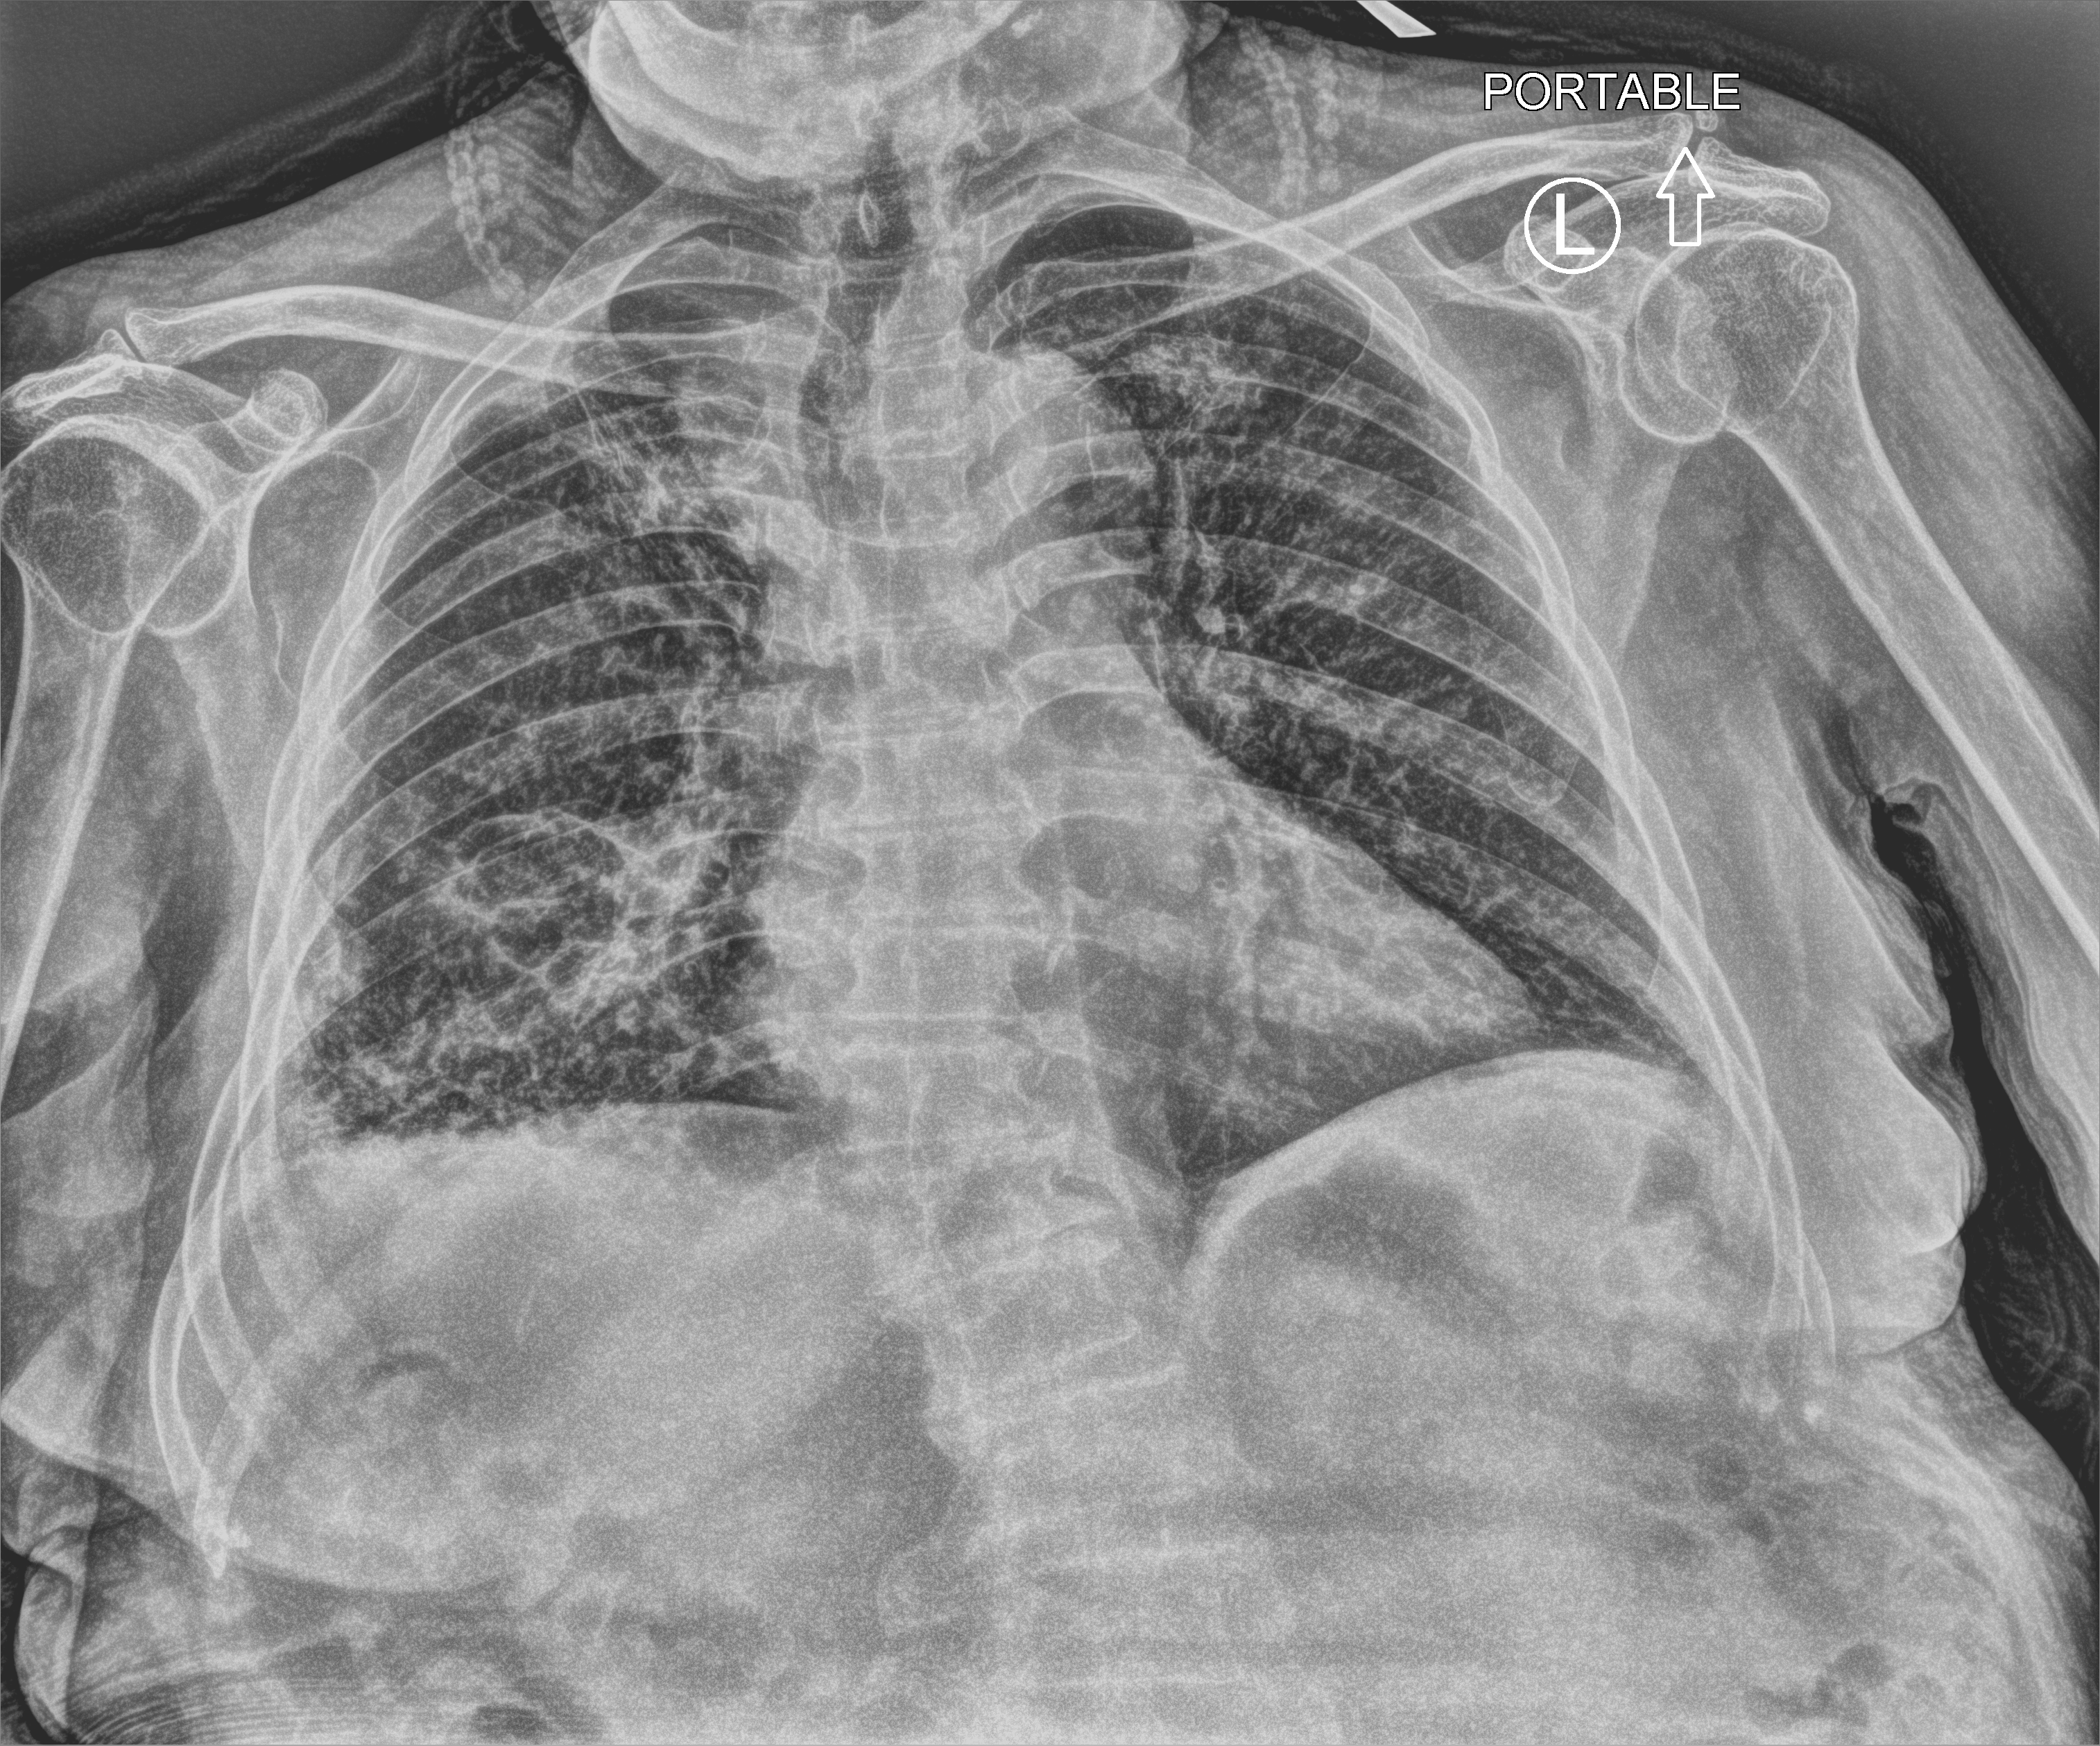
Chest X-ray (portable), anteroposterior (AP) projection. Patient hospitalised with COVID-19; female, aged 75–90 years.
Admission-level facts for this patient (not findings on this image; timing relative to this image not recorded): admitted to intensive care during this hospital stay: no; mechanically ventilated during this hospital stay: no.